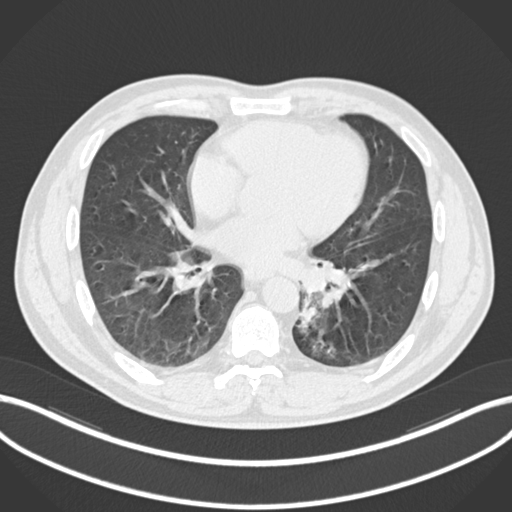
Chest CT, one axial slice. Position 96 of 223 along the scan axis. Reconstruction kernel B30f. 120 kVp. Lung window (W 1500 / L -600 HU). 1 mm slice thickness. 512 × 512 image matrix, field of view 400 × 400 mm. Patient: male, 50 years. From the clinical record (not read from this slice): clinical TNM (as recorded): T2a N3 M0.
Outlined on this slice (rectangle marked by the reading radiologist):
- lung tumour (recorded histology: squamous cell carcinoma): box from (x=297, y=297) to (x=318, y=337) px